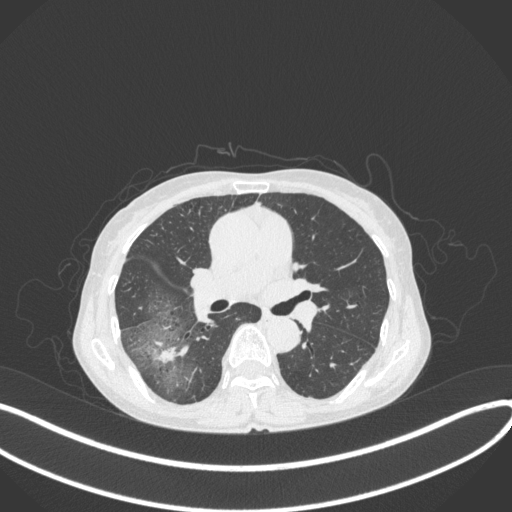
Chest CT, one axial slice. Slice 226 of 379 in the series (ordered by position). Reconstruction kernel B31f. 120 kVp. Lung window (W 1500 / L -600 HU). 1 mm slice thickness. 512 × 512 image matrix, field of view 400 × 400 mm. Patient: female, 69 years. From the clinical record (not read from this slice): clinical TNM (as recorded): T1b N0 M0; histopathological grade: G2-3.
Outlined on this slice (rectangle marked by the reading radiologist):
- lung tumour (recorded histology: adenocarcinoma): bounding box (x1, y1, x2, y2) in pixels: (150, 336, 193, 373)